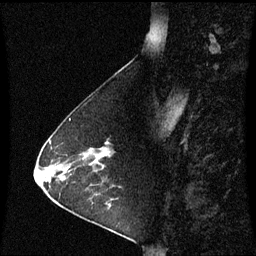
Breast MRI (dynamic contrast-enhanced), one sagittal slice; position 21 of 60 along the scan axis; dynamic contrast-enhanced series, image 2 of 3 at this slice position (ordered by acquisition); 1.5 T; TE 4.2 ms, TR 8.9 ms; 256 × 256 image matrix. Patient: female, 63 years. Case-level facts recorded for this patient, not image findings: setting: breast cancer imaged before/during neoadjuvant chemotherapy; receptor status: HR-positive, HER2-negative.
Structures marked on this image (semi-automatic segmentation, software-assisted and operator-edited):
- analysis volume of interest (the breast-tissue region the enhancement analysis was run in; not a lesion): box from (x=76, y=139) to (x=113, y=173) px
- tumour enhancement mask (voxels above the 70 % enhancement threshold inside the analysis volume of interest): (x=96, y=153)–(x=112, y=159)